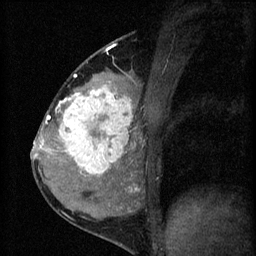
Breast MRI (dynamic contrast-enhanced), one sagittal slice; 3 images stored at this slice position (order not interpretable as contrast timing); 1.5 T; TE 4.2 ms, TR 8.2 ms; 2 mm slice thickness; 256 × 256 image matrix, field of view 180 × 180 mm. Patient: female, 37 years.
Annotated regions visible in this slice (semi-automatic segmentation, software-assisted and operator-edited):
- analysis volume of interest (the breast-tissue region the enhancement analysis was run in; not a lesion): bounding box [x1, y1, x2, y2] px = [53, 78, 140, 181]
- tumour enhancement mask (voxels above the 70 % enhancement threshold inside the analysis volume of interest): [55, 78, 133, 177]